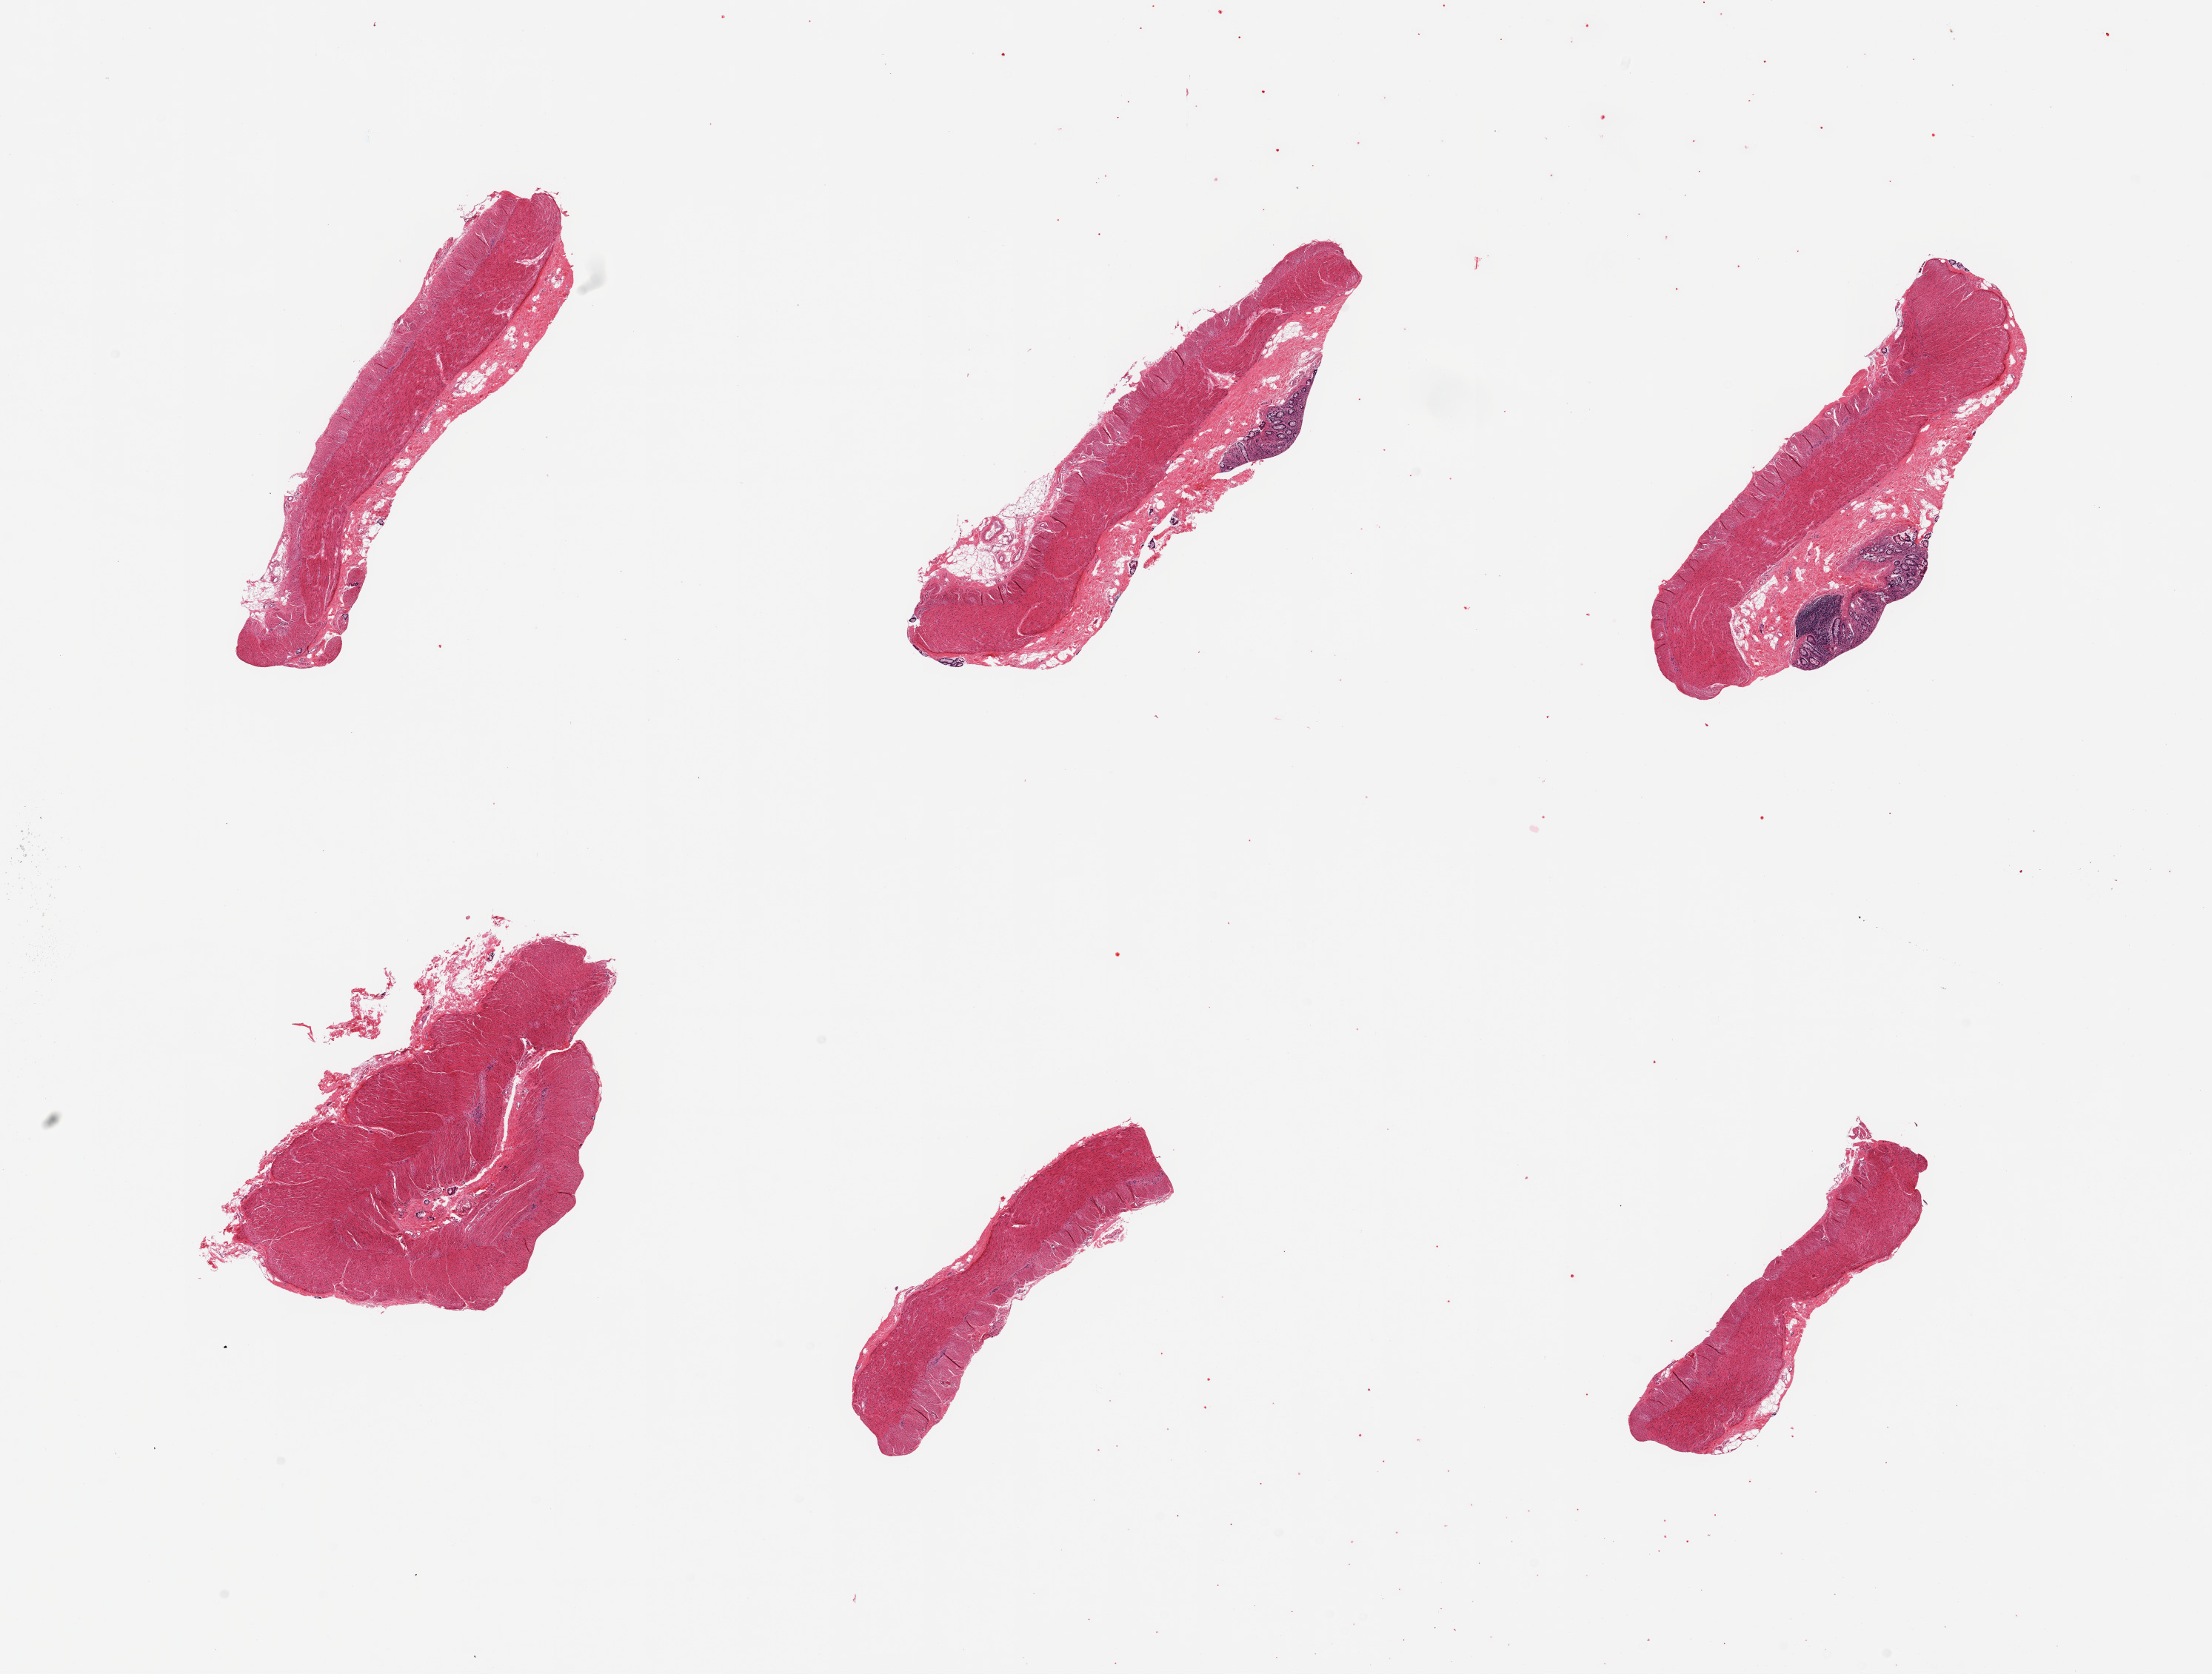
Hematoxylin and eosin (H&E) whole-slide image, low-resolution overview of the scanned area, about 23.6 x 17.9 mm (slide scanned at 20x). PAXgene-fixed, paraffin-embedded tissue. Sampled site (target tissue): transverse colon. Donor tissue sample. Male donor.
* pathologist's review note for this sample: 6 pieces; predominantly muscularis, 2 pieces include small portion of mucosa